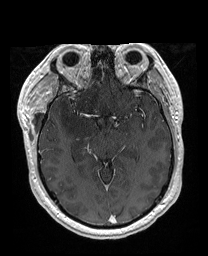
Brain MRI from a brain-tumour surgery series, one axial slice; position 107 of 176 along the scan axis; T1-weighted post-contrast; 1 mm slice thickness; 208 × 256 image matrix, field of view 208 × 256 mm. Case-level facts recorded for this patient, not image findings: histopathology: Astrocytoma; WHO grade: 4.
Annotated regions visible in this slice (manually delineated by an expert):
- previous resection cavity: bounding box (x1, y1, x2, y2) in pixels: (56, 61, 106, 73)